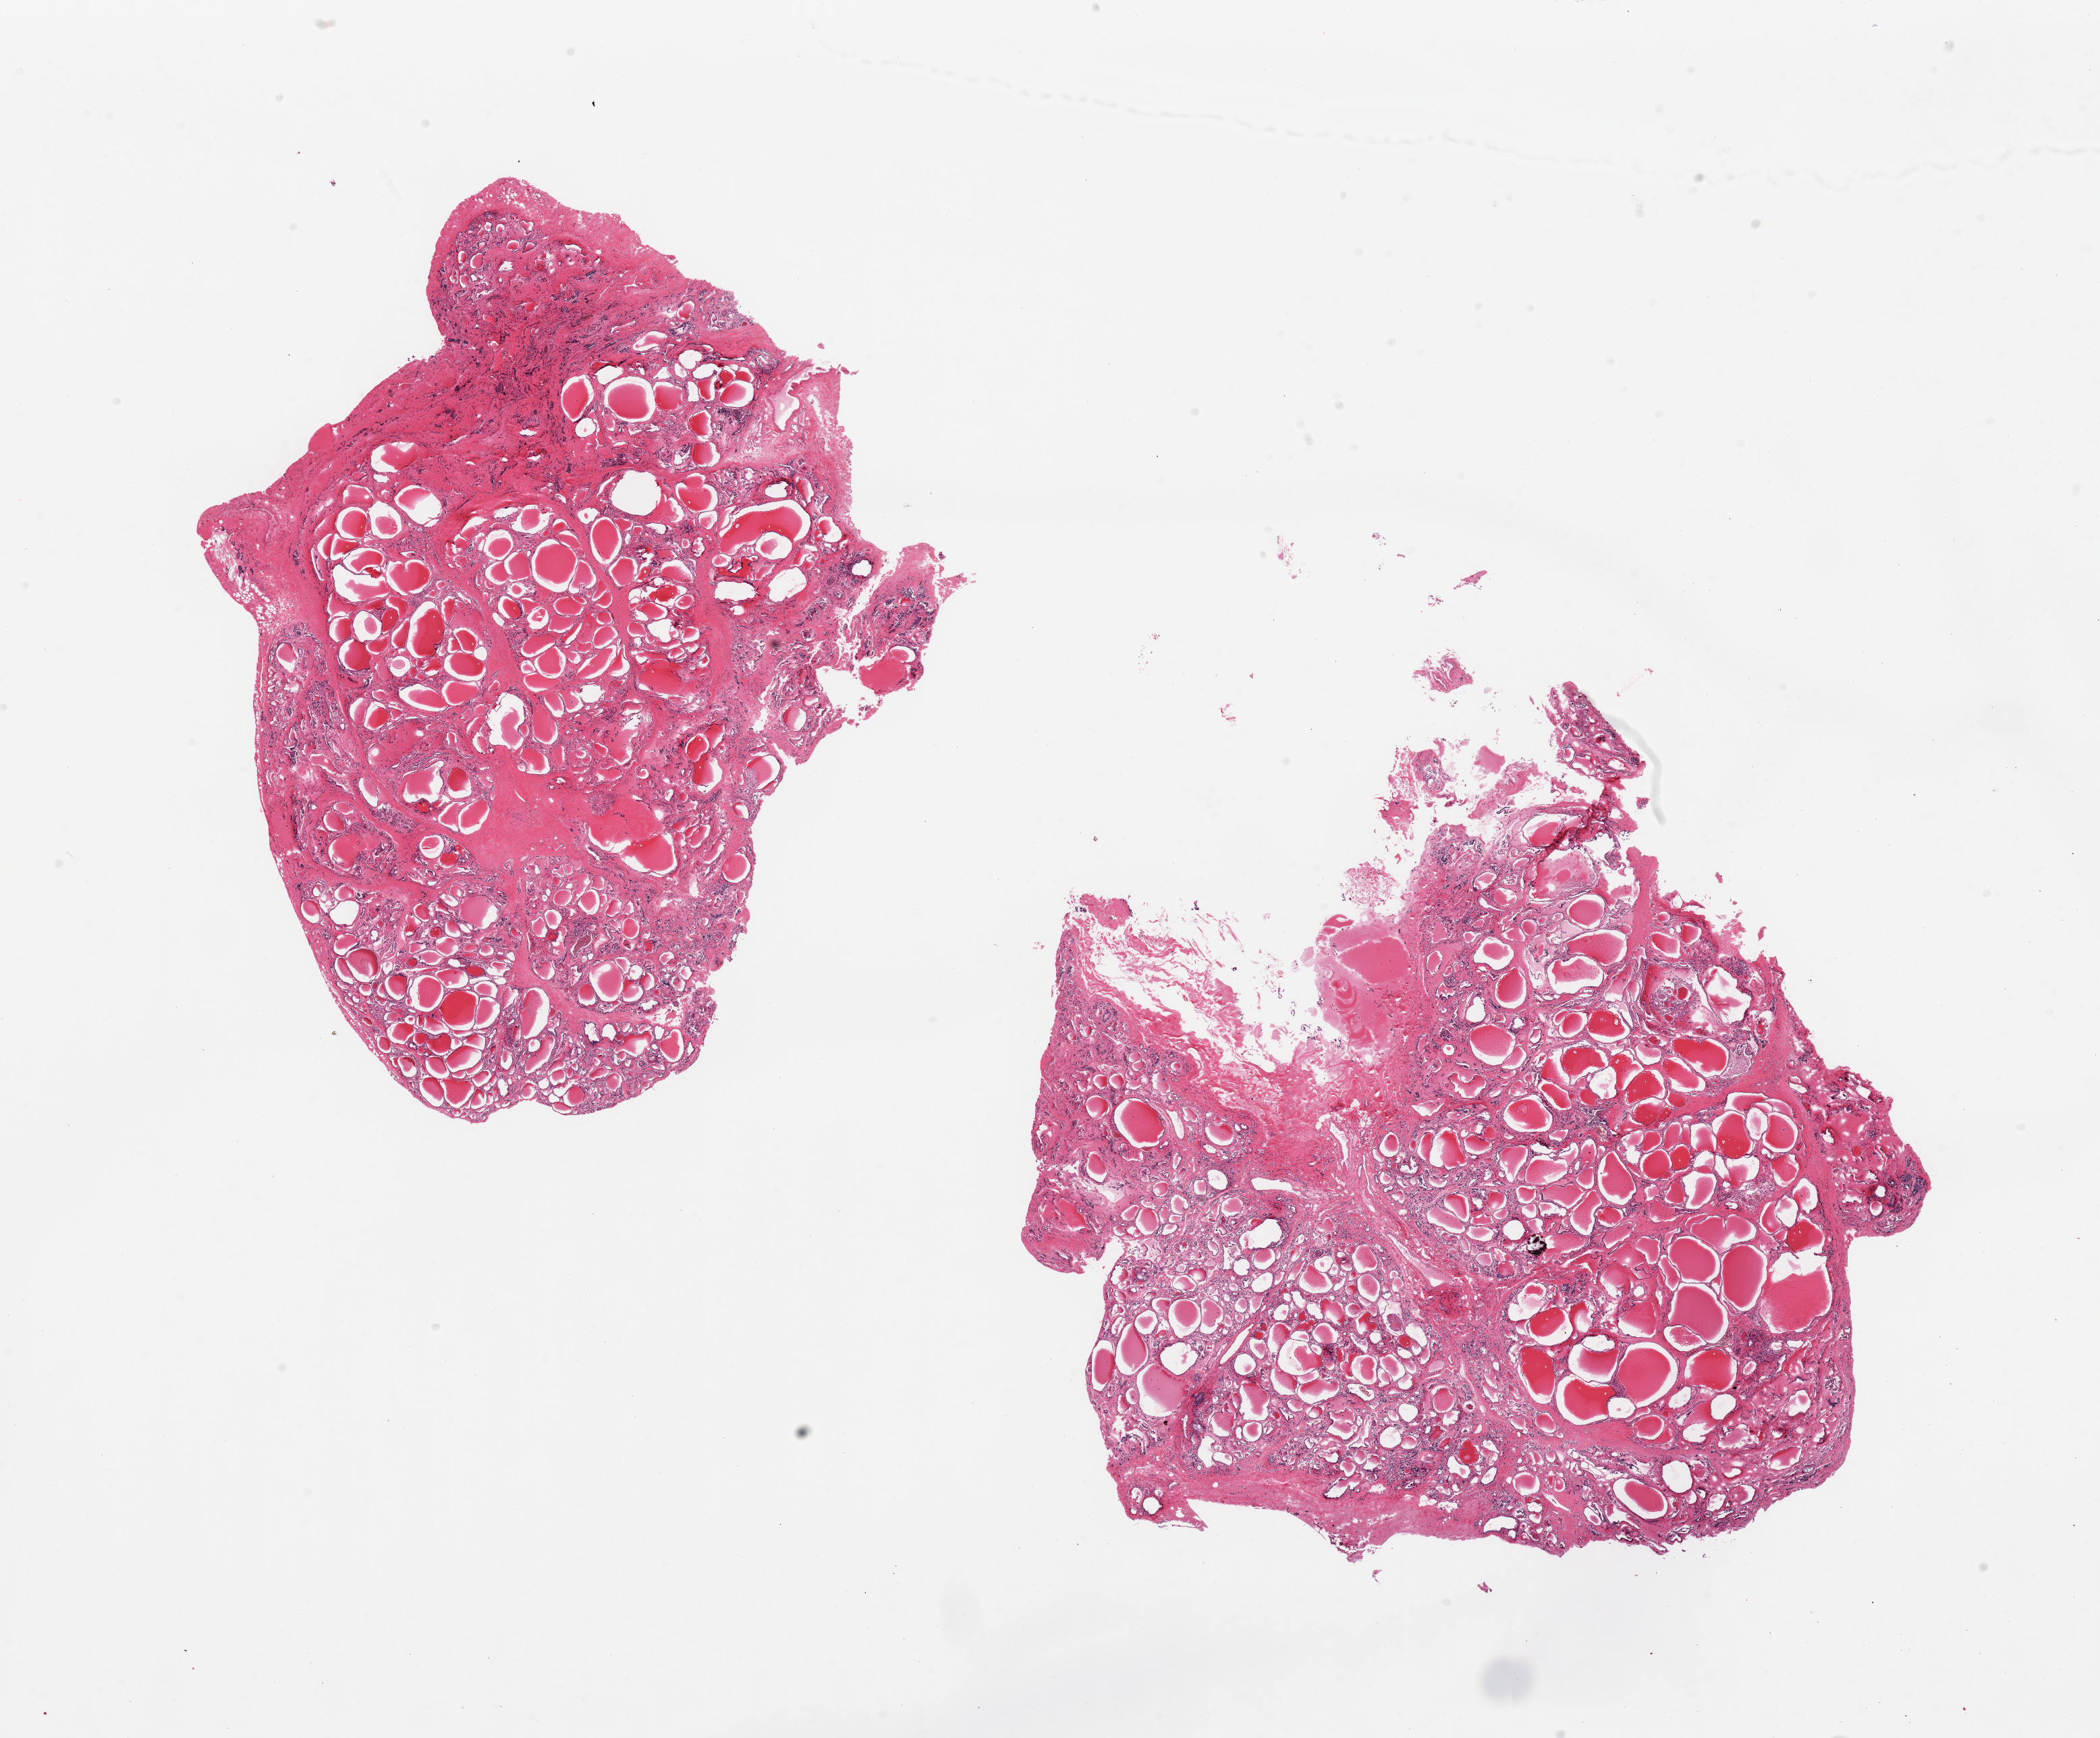
Digitized haematoxylin and eosin-stained section, shown as a low-resolution overview of the whole scanned area (about 24.6 x 20.4 mm). PAXgene-fixed, paraffin-embedded tissue. Sampled site (target tissue): thyroid. Tissue donor sample. Male donor.
• reviewer comment on this tissue sample: 2 pieces; interstitial fibrosis and variably sized micro nodules; focal calcification